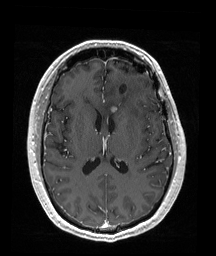
Brain MRI from a brain-tumour surgery series, one axial slice. Slice 88 of 192 in the series (ordered by position). T1-weighted post-contrast. 1 mm slice thickness. 216 × 256 image matrix, field of view 211 × 250 mm. Case-level facts recorded for this patient, not image findings: histopathology: Oligodendroglioma; WHO grade: 2; IDH mutation: yes.
Structures marked on this image (expert manual segmentation):
- tumour: bounding box <112,107,116,111> (left, top, right, bottom; pixels)